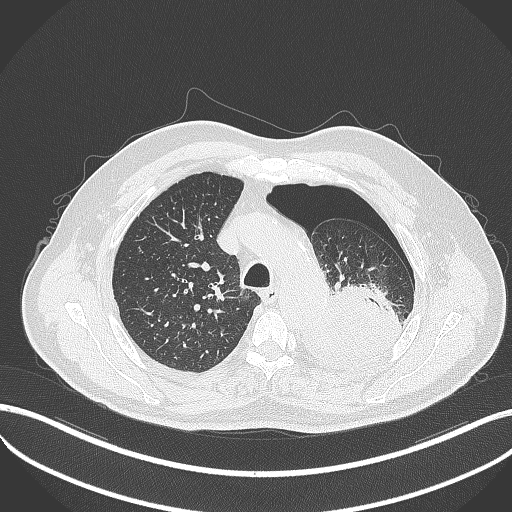
Chest CT, one axial slice; slice 382 of 464 in the series (ordered by position); reconstruction kernel B70f; 120 kVp; lung window (W 1500 / L -600 HU); 1 mm slice thickness; 512 × 512 image matrix, field of view 400 × 400 mm. Patient: male, 76 years. Case-level facts recorded for this patient, not image findings: clinical TNM (as recorded): T3 N0 M1b.
Outlined on this slice (bounding box drawn by a radiologist):
- lung tumour (recorded histology: adenocarcinoma): bounding box [x1, y1, x2, y2] px = [294, 279, 404, 375]